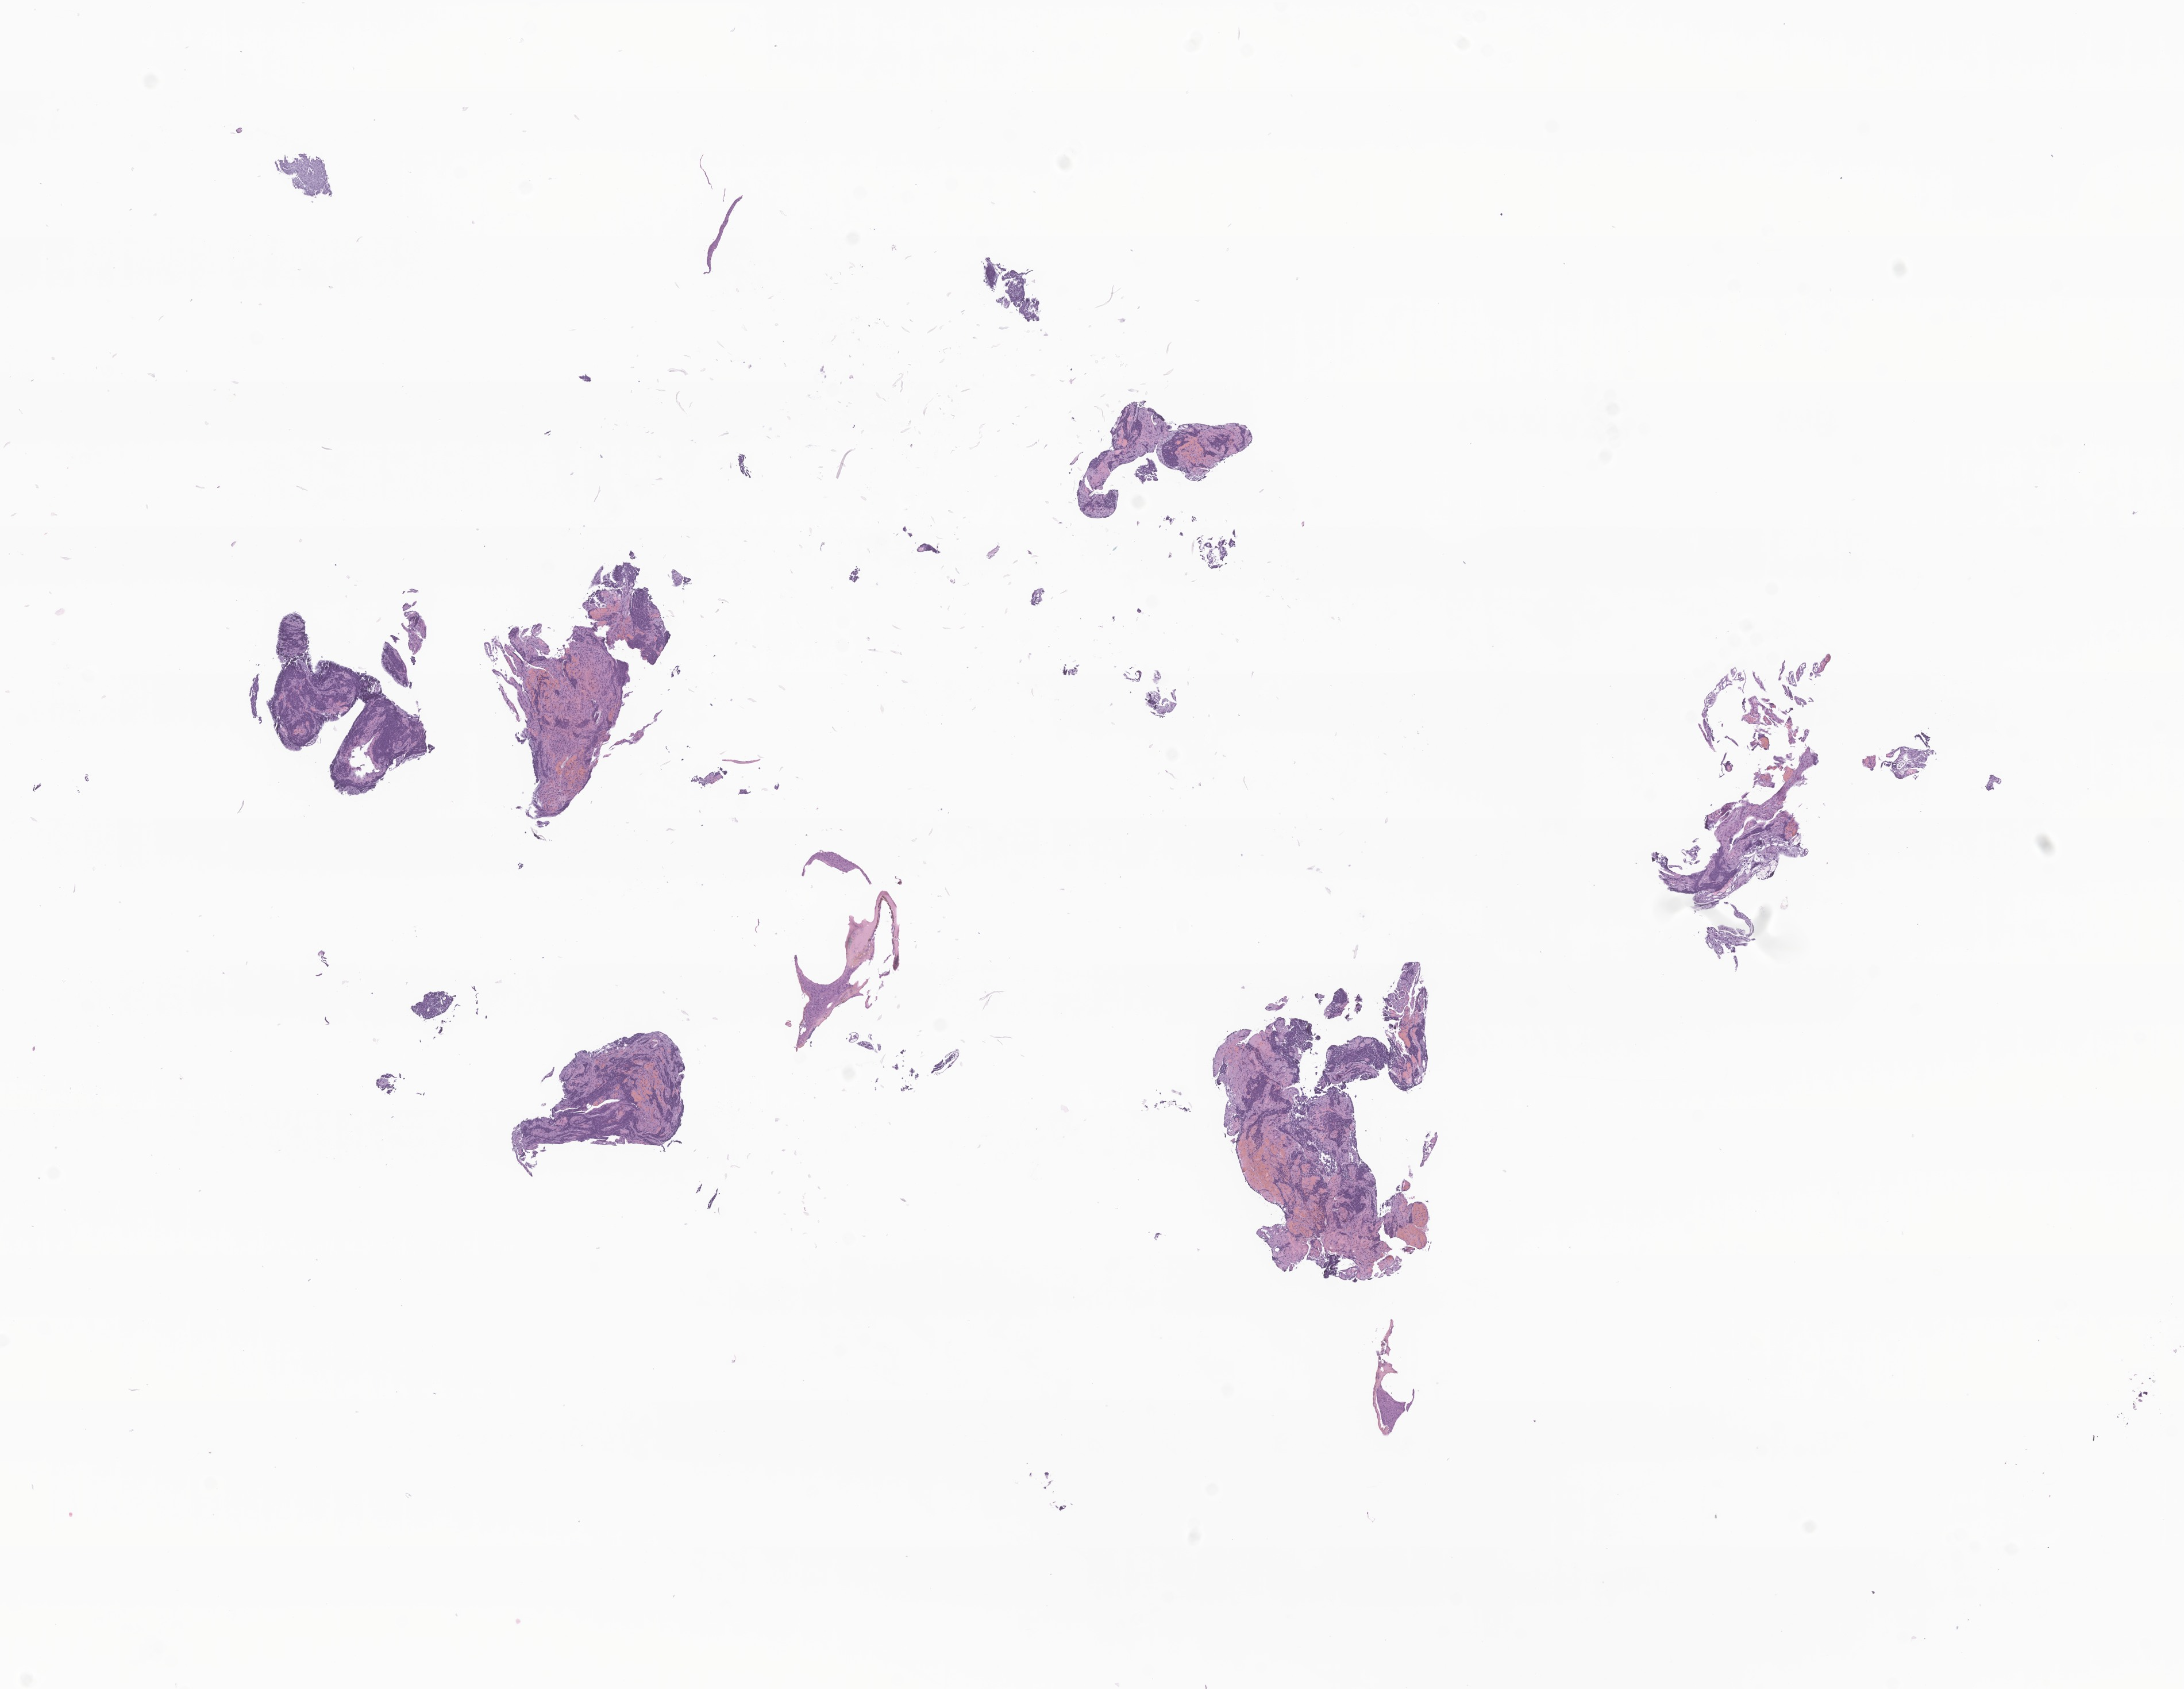
Digitized haematoxylin and eosin-stained section of tumor tissue from the brain, whole scanned area (about 16.0 x 12.4 mm) shown as a low-resolution overview. FFPE section. Male patient, age 449 days (about 1.2 years).
Diagnosis: Glioma, malignant.